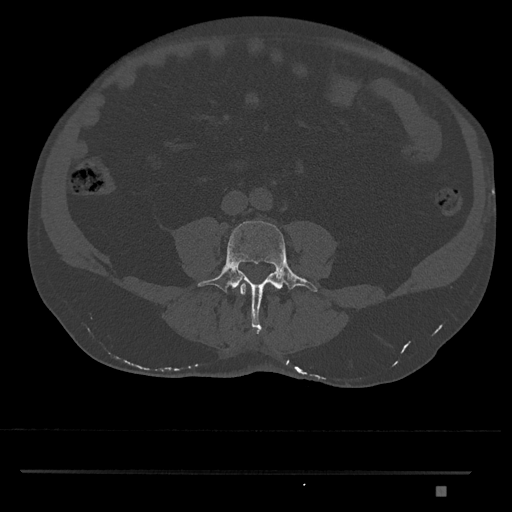
CT including the spine, one axial slice; slice 623 of 1134 in the series (ordered by position); 120 kVp; bone window (W 1800 / L 400 HU); 0.5 mm slice thickness; 512 × 512 image matrix, field of view 429 × 429 mm. Male patient, age 65 years. Case-level facts recorded for this patient, not image findings: primary cancer: prostate.
Outlined on this slice (semi-automatic segmentation, software-assisted and operator-edited):
- L3 vertebra: bounding box <239,283,277,295> (left, top, right, bottom; pixels)
- L4 vertebra: <197,220,317,334>